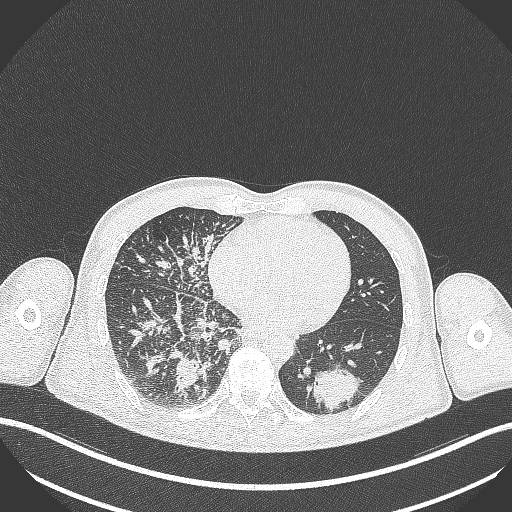
Chest CT, one axial slice. Position 115 of 348 along the scan axis. Lung window (W 1500 / L -600 HU). 1 mm slice thickness. 512 × 512 image matrix, field of view 400 × 400 mm. Male patient, age 49 years. Case-level facts recorded for this patient, not image findings: clinical TNM (as recorded): T2b N1 M0.
Outlined on this slice (rectangle marked by the reading radiologist):
- lung tumour (recorded histology: adenocarcinoma): bounding box (x1, y1, x2, y2) in pixels: (304, 364, 364, 411)